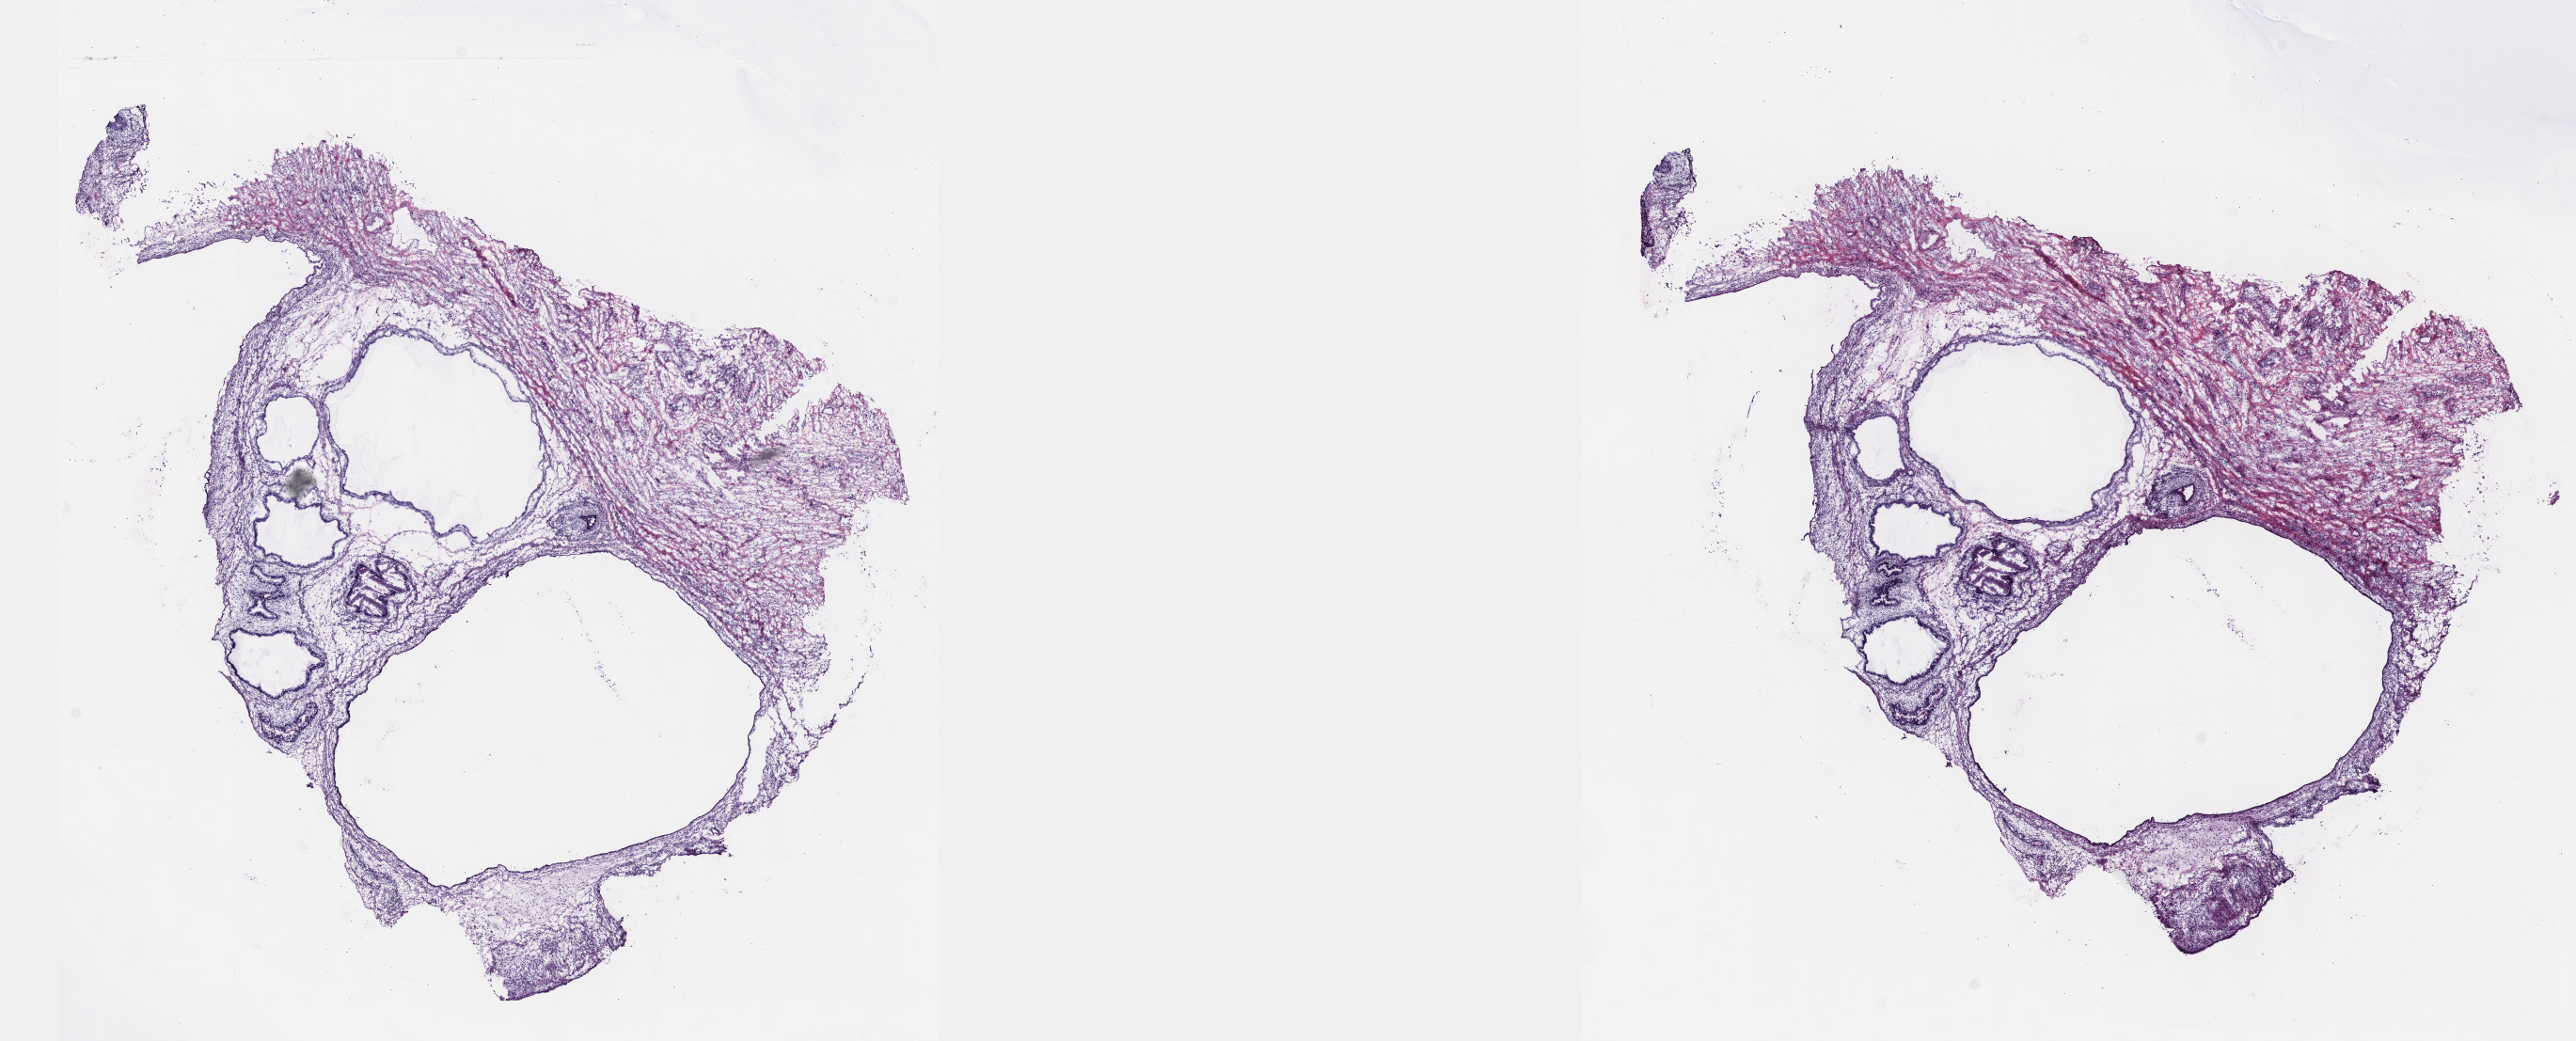
Digitized H&E-stained tissue section (whole slide) — whole scanned area (about 22.1 x 8.9 mm) shown as a low-resolution overview. Patient sex: male. Composition of this section per pathologist review: tumour cells 100%, tumour nuclei 80%, normal cells 0%, stromal cells 0%, necrosis 0%. Inflammatory infiltration, as recorded: lymphocyte infiltration 2%, monocyte infiltration 0%, neutrophil infiltration 0%.
- specimen: frozen section; primary tumour sample from the testis